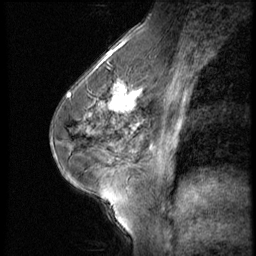
Breast MRI (dynamic contrast-enhanced), one sagittal slice; 3 images stored at this slice position (order not interpretable as contrast timing); 1.5 T; TE 4.2 ms, TR 9 ms; 2.5 mm slice thickness; 256 × 256 image matrix. Female patient, age 45 years. Case-level facts recorded for this patient, not image findings: setting: breast cancer imaged before/during neoadjuvant chemotherapy; receptor status: HR-positive, HER2-negative.
Outlined on this slice (semi-automatically segmented with operator editing):
- analysis volume of interest (the breast-tissue region the enhancement analysis was run in; not a lesion): bounding box <102,77,166,129> (left, top, right, bottom; pixels)
- tumour enhancement mask (voxels above the 140 % enhancement threshold inside the analysis volume of interest): <107,80,145,129>